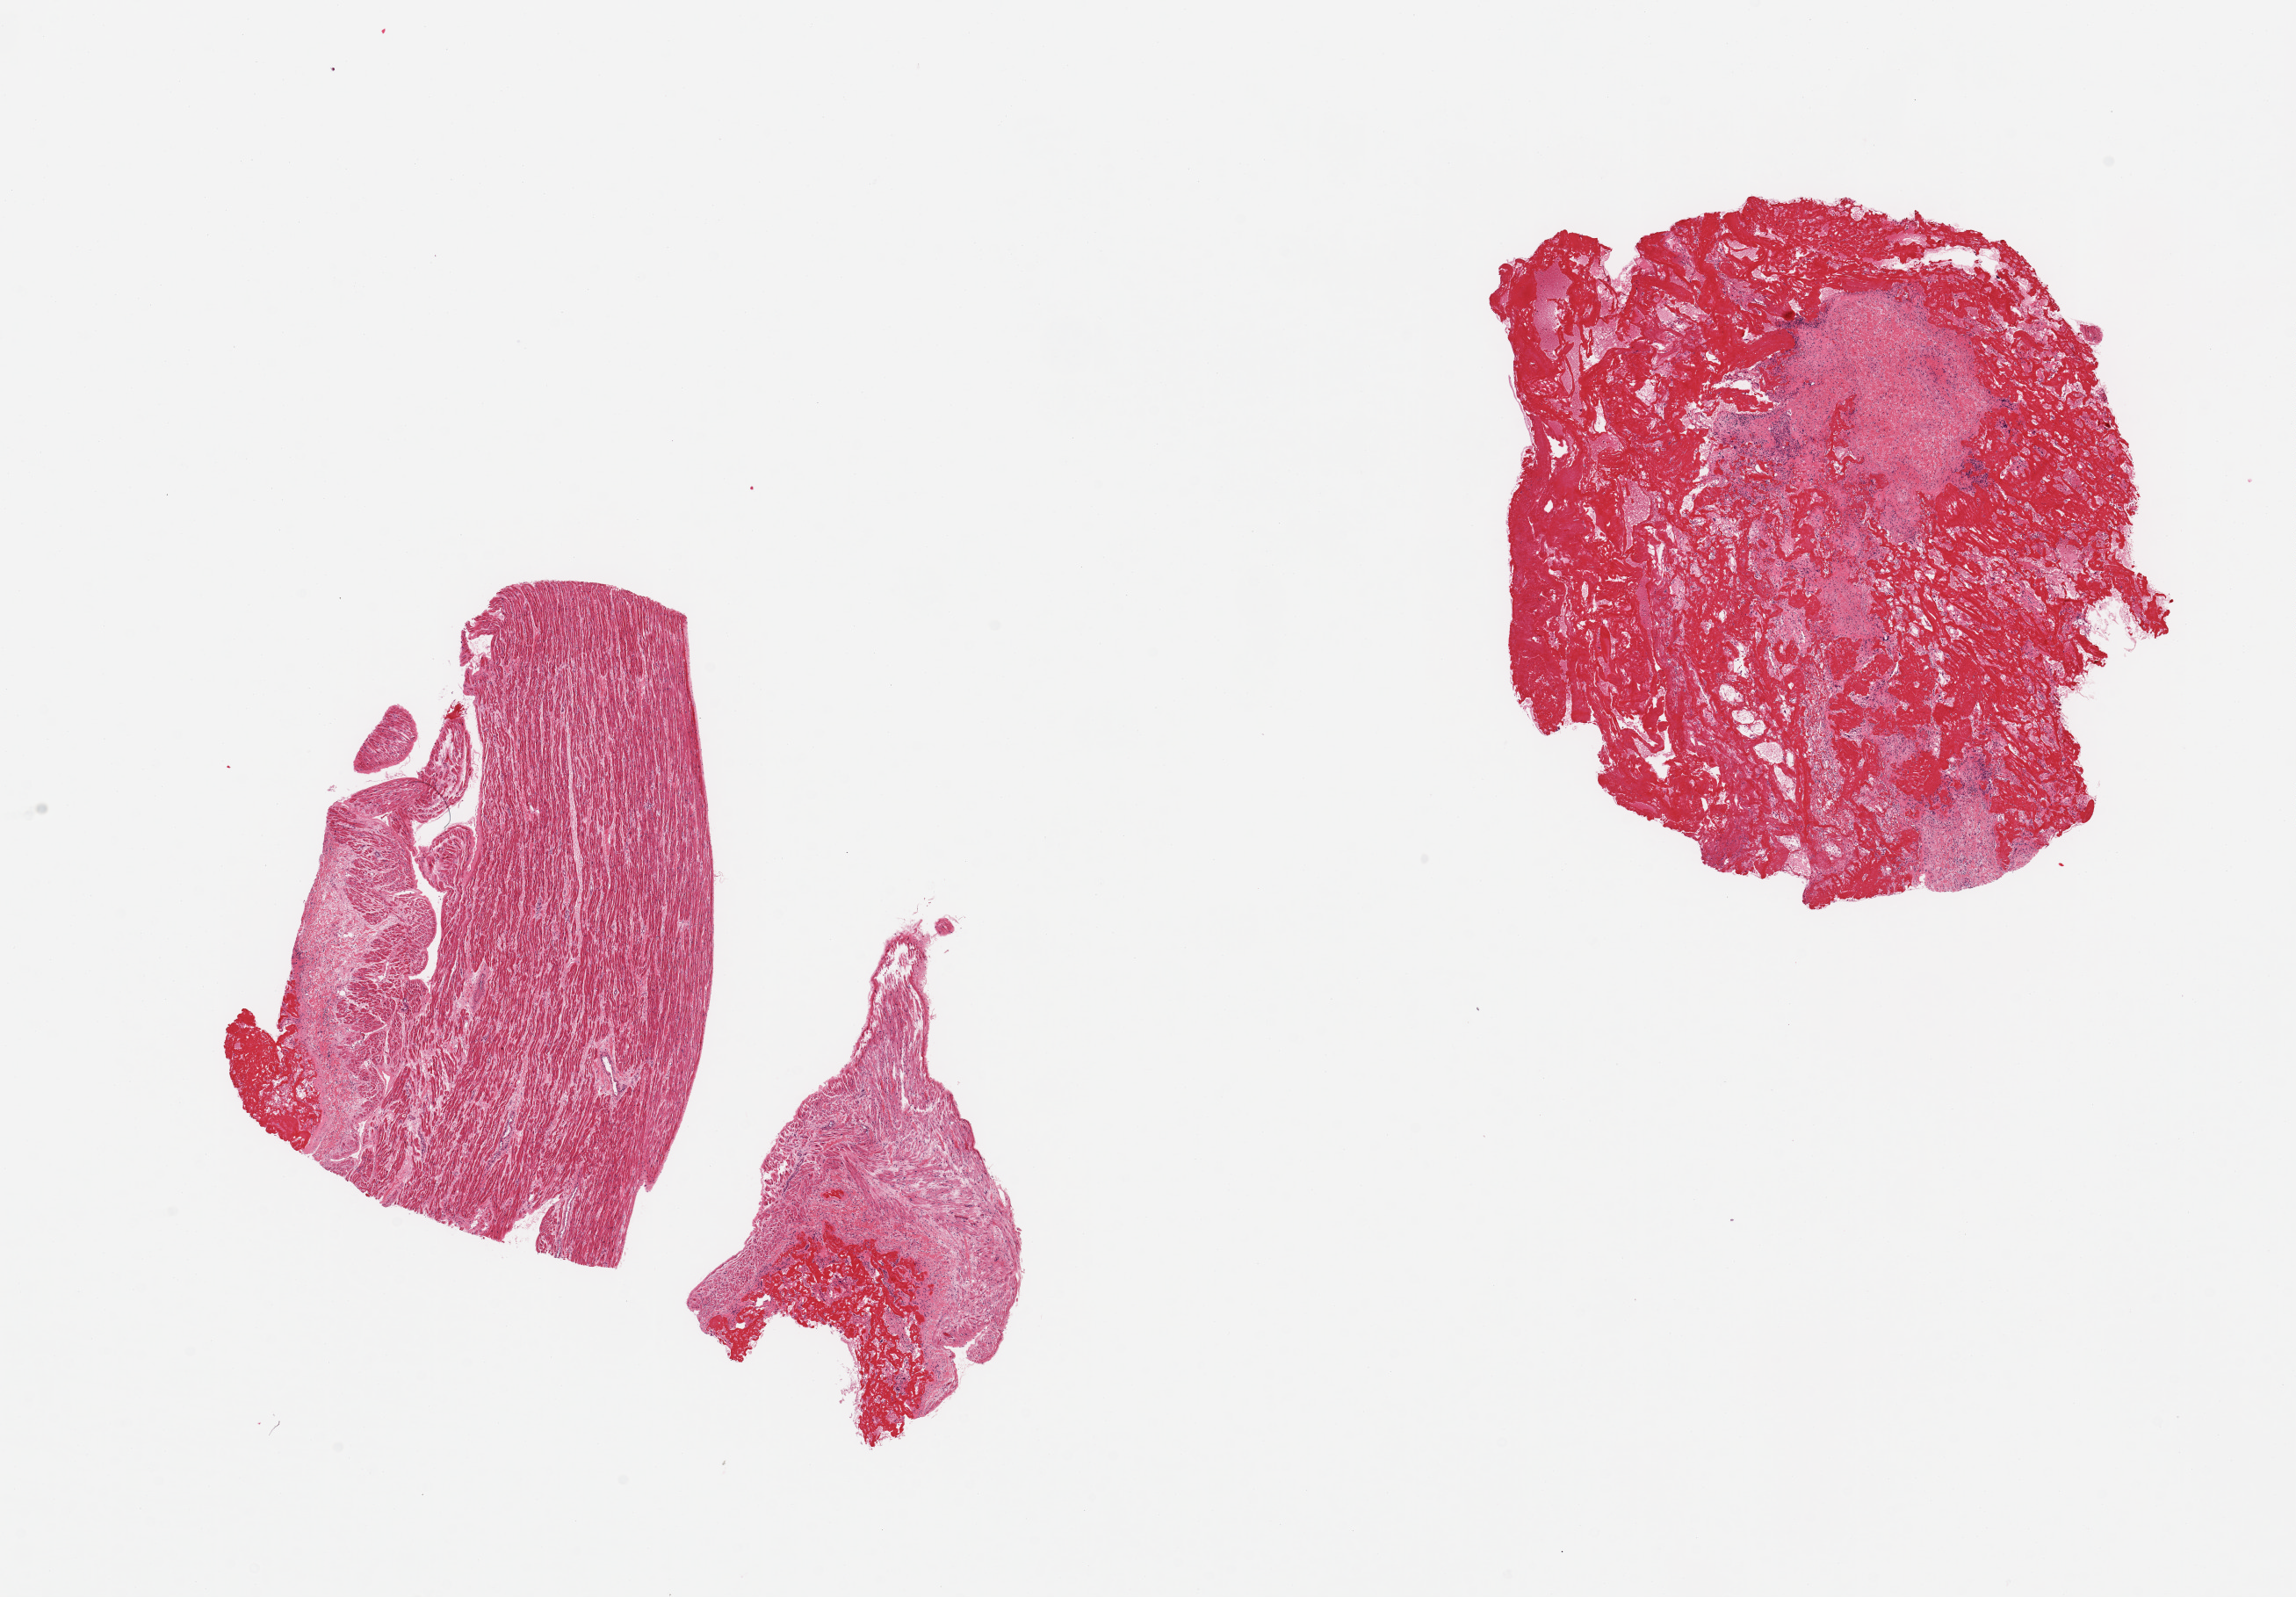
Whole-slide image, H&E stain, brightfield, a low-resolution overview of the entire scanned area, about 20.7 x 14.4 mm (from a 20x scan); PAXgene-fixed, paraffin-embedded tissue; target tissue: auricular appendage; tissue donor sample.
Reviewer comment on this tissue sample: 2 pieces, ~40-50% clot.